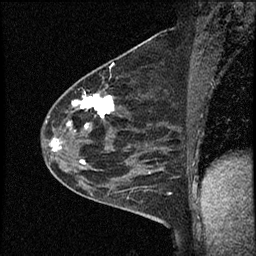
Breast MRI (dynamic contrast-enhanced), one sagittal slice; position 40 of 60 along the scan axis; dynamic contrast-enhanced study with each time point stored as its own series, time point 2 of 4 at this slice position (early post-contrast, ordered by acquisition time); 1.5 T; TE 4.2 ms, TR 17.6 ms; 2 mm slice thickness; 256 × 256 image matrix, field of view 200 × 200 mm. Female patient, age 53 years. From the clinical record (not read from this slice): setting: breast cancer imaged before/during neoadjuvant chemotherapy; receptor status: HR-positive, HER2-negative.
Structures marked on this image (semi-automatic segmentation, software-assisted and operator-edited):
- analysis volume of interest (the breast-tissue region the enhancement analysis was run in; not a lesion): bounding box <42,69,156,199> (left, top, right, bottom; pixels)
- tumour enhancement mask (voxels above the 100 % enhancement threshold inside the analysis volume of interest): <52,93,115,163>